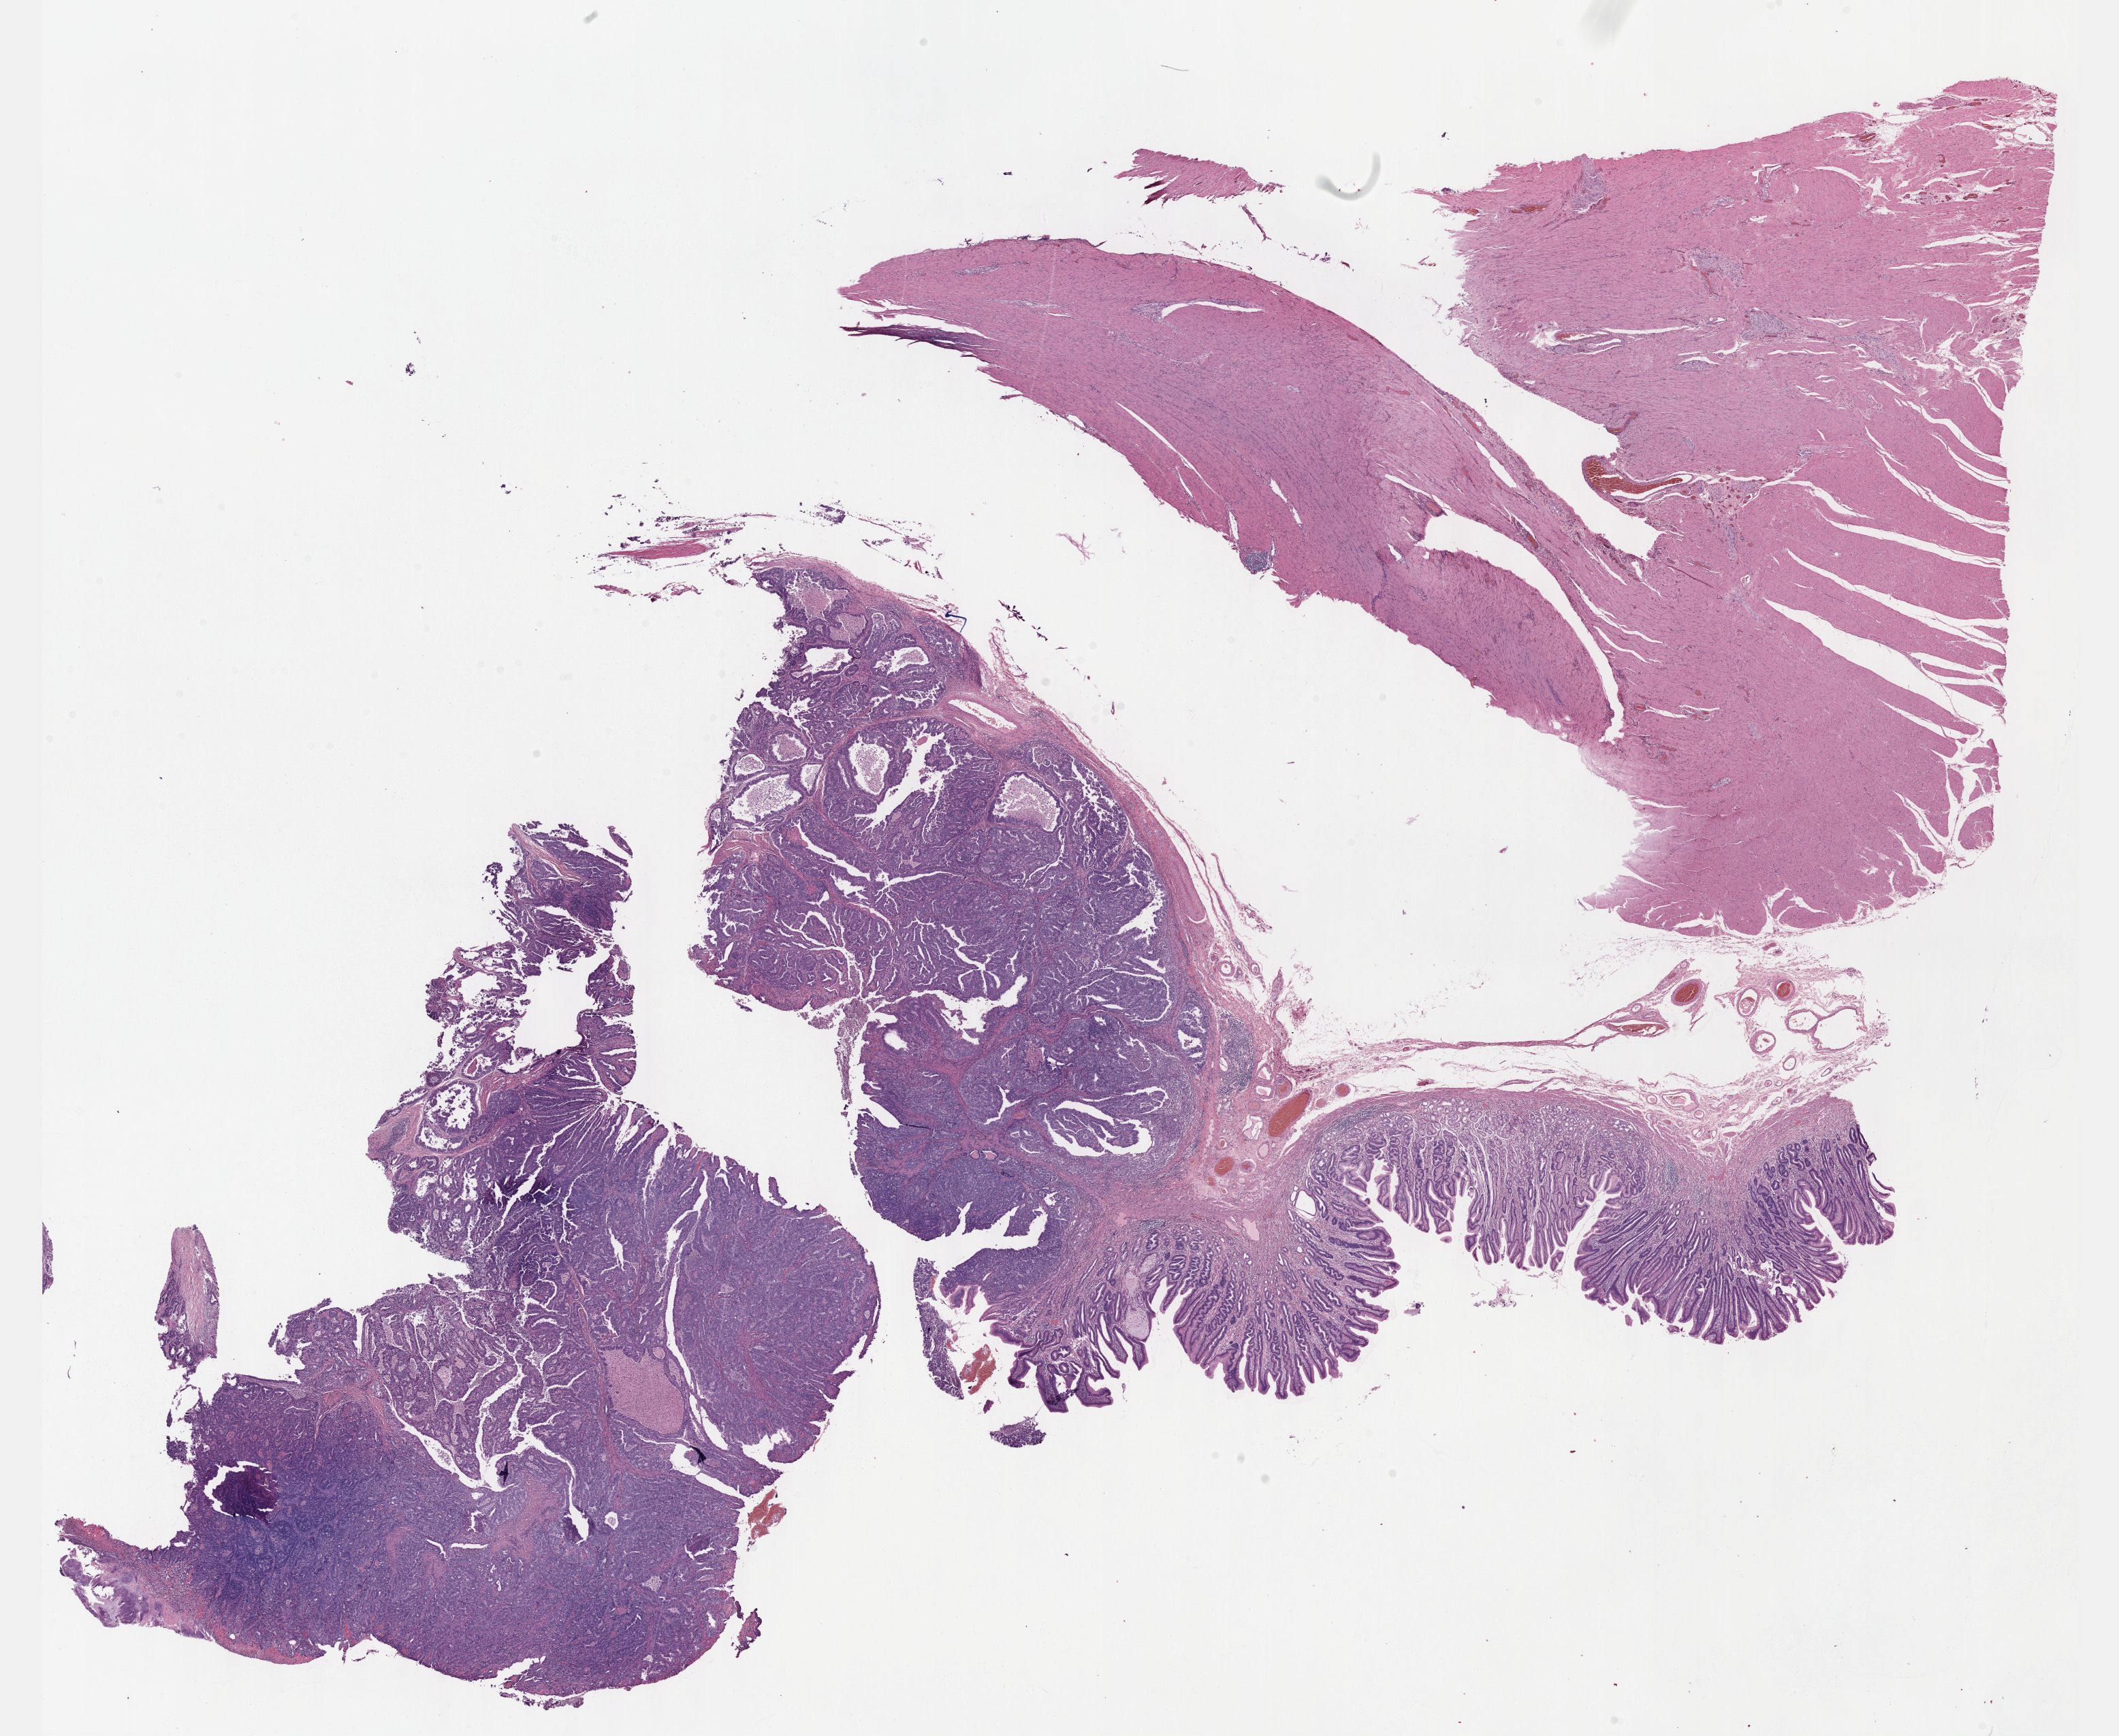
H&E whole-slide image — whole scanned area (about 25.1 x 20.6 mm, from a 40x scan) shown as a low-resolution overview, FFPE section, primary tumour sample from the stomach. Female, age 67 years at initial diagnosis. Histologic grade: G2 (moderately differentiated).
AJCC pathologic stage: IIIA. Histologic diagnosis: Tubular adenocarcinoma (gastric antrum).